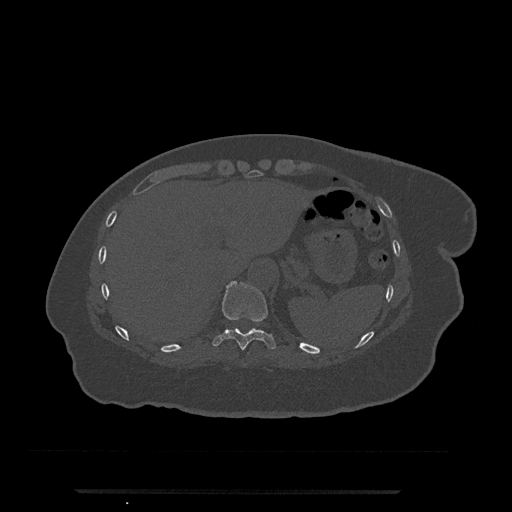
CT including the spine, one axial slice; position 281 of 797 along the scan axis; reconstruction kernel Br40s/3; 120 kVp; bone window (W 1800 / L 400 HU); 0.5 mm slice thickness; 512 × 512 image matrix. Patient: female, 51 years. From the clinical record (not read from this slice): primary cancer: neuro; vertebrae with lytic lesions (as recorded): T8.
Structures marked on this image (semi-automatically segmented with operator editing):
- T10 vertebra: bounding box (x1, y1, x2, y2) in pixels: (212, 281, 276, 350)